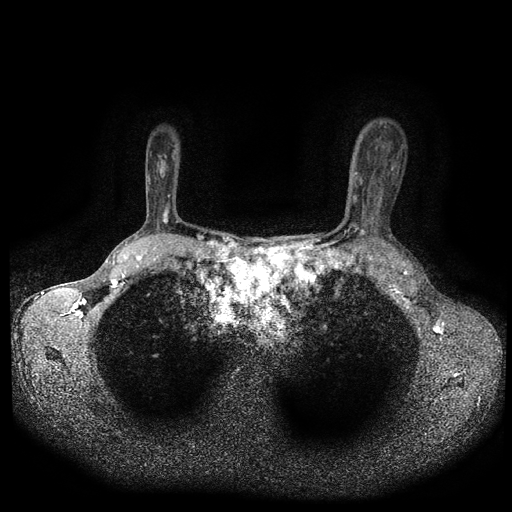
Breast MRI (dynamic contrast-enhanced, multi-phase), one axial slice. Position 75 of 116 along the scan axis. Dynamic contrast-enhanced series, time point 2 of 5 at this slice position (early post-contrast). 1.5 T. TE 2.7 ms, TR 5.4 ms. 2 mm slice thickness. 512 × 512 image matrix. Female patient, age 49 years.
Outlined on this slice (semi-automatically segmented with operator editing):
- breast lesion (labelled benign in the annotation): bounding box <158,153,168,180> (left, top, right, bottom; pixels)